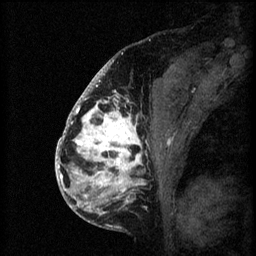
Breast MRI (dynamic contrast-enhanced), one sagittal slice; position 31 of 60 along the scan axis; 3 images stored at this slice position (order not interpretable as contrast timing); 1.5 T; TE 4.2 ms, TR 8.2 ms; 2 mm slice thickness; 256 × 256 image matrix. Patient: female, 41 years.
Annotated regions visible in this slice (semi-automatic segmentation, software-assisted and operator-edited):
- analysis volume of interest (the breast-tissue region the enhancement analysis was run in; not a lesion): bounding box (x1, y1, x2, y2) in pixels: (72, 108, 172, 205)
- tumour enhancement mask (voxels above the 70 % enhancement threshold inside the analysis volume of interest): (72, 108, 170, 205)